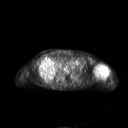
FDG PET of an extremity soft-tissue mass (from a PET/CT study), one axial slice. Slice 144 of 267 in the series (ordered by position). 3.27 mm slice thickness. 128 × 128 image matrix, field of view 700 × 700 mm. Patient: female, 83 years. Case-level facts recorded for this patient, not image findings: histological type: pleiomorphic leiomyosarcoma; grade: high; site of the primary tumour: left biceps.
Structures marked on this image (expert contour drawn on MRI and transferred to this co-registered scan by the dataset authors):
- gross tumour volume including surrounding oedema: bounding box [x1, y1, x2, y2] px = [94, 65, 108, 76]
- gross tumour volume (mass): [94, 65, 107, 75]